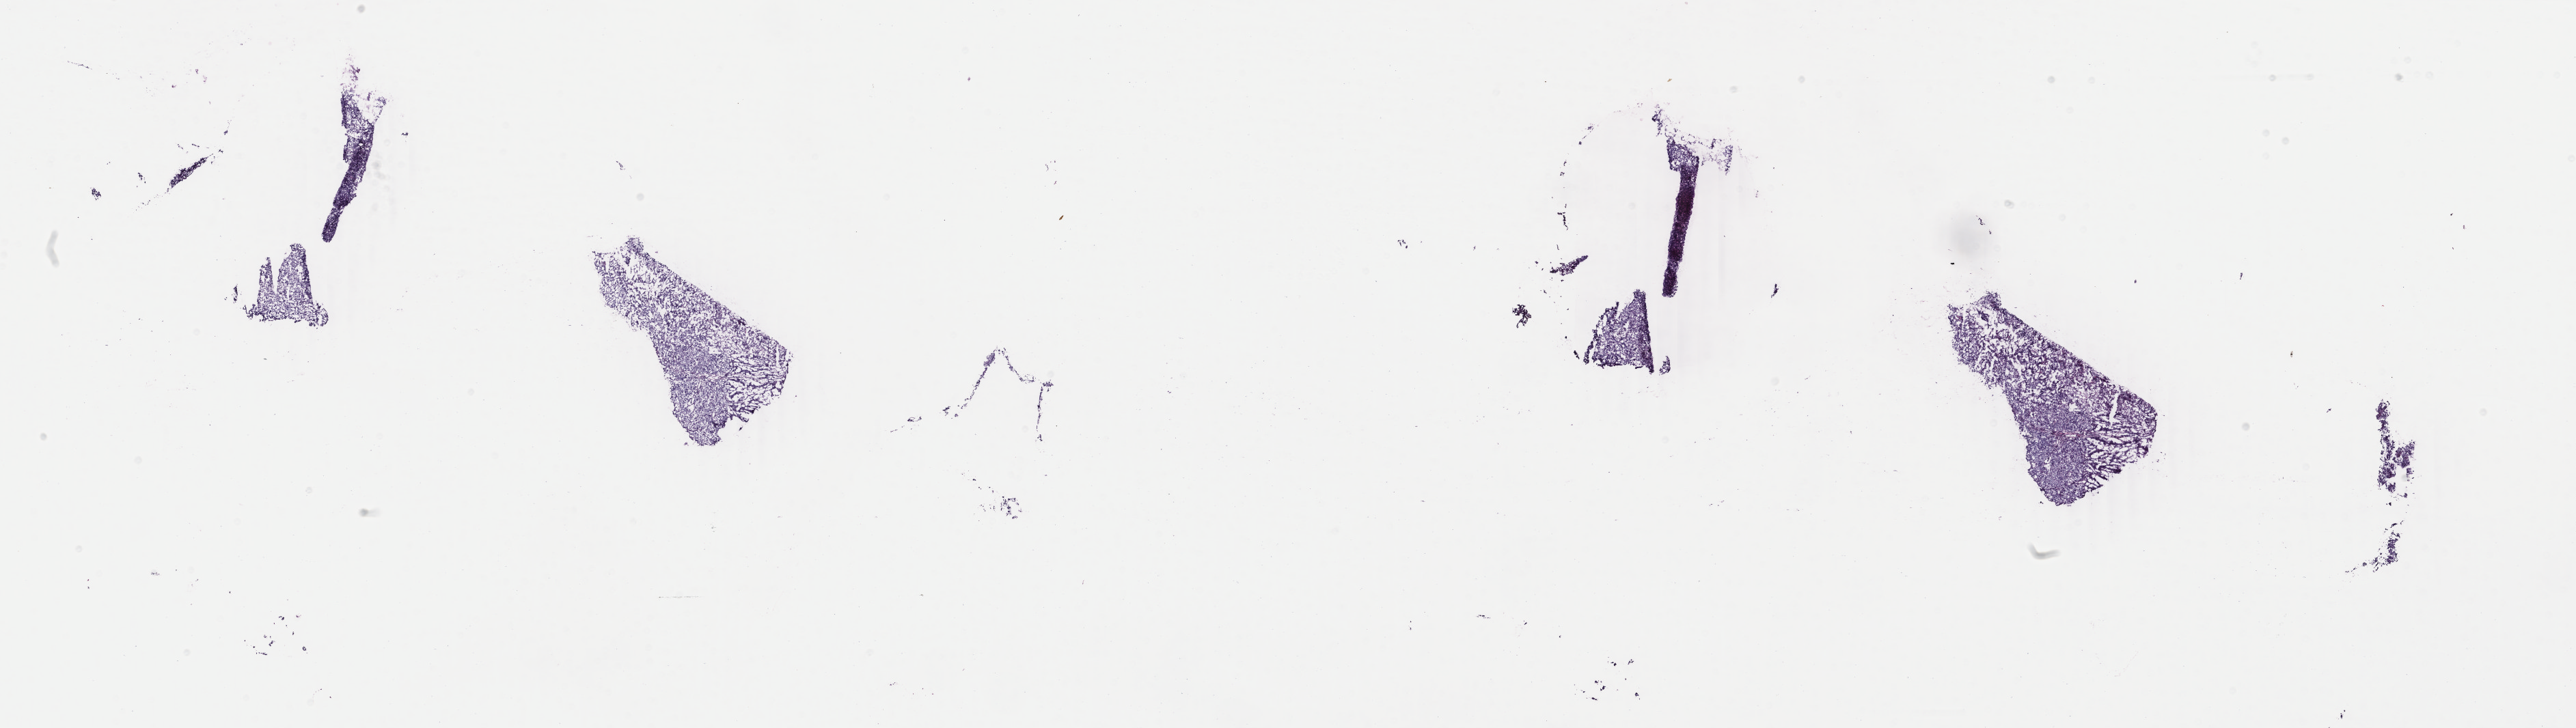
Hematoxylin and eosin (H&E) stained whole-slide image — shown as a low-resolution overview of the whole scanned area (about 30.0 x 8.5 mm). Frozen section from the bottom of the tissue portion. Primary tumour sample from the uterus. Female patient; age at initial diagnosis 64 years. Slide review estimates, as recorded: tumour cells 100%, tumour nuclei 98%.
Pathologic diagnosis: Endometrioid adenocarcinoma, NOS (endometrium).